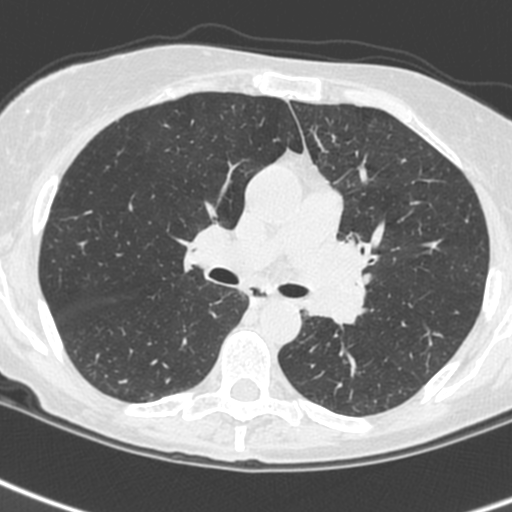
Low-dose screening chest CT, one axial slice; slice 149 of 242 in the series (ordered by position); lung window (W 1500 / L -600 HU); 1.3 mm slice thickness; 512 × 512 image matrix.
Annotated regions visible in this slice (expert manual segmentation):
- lesion 3 (tumor, upper lobe of left lung): bounding box [x1, y1, x2, y2] px = [306, 240, 370, 326]